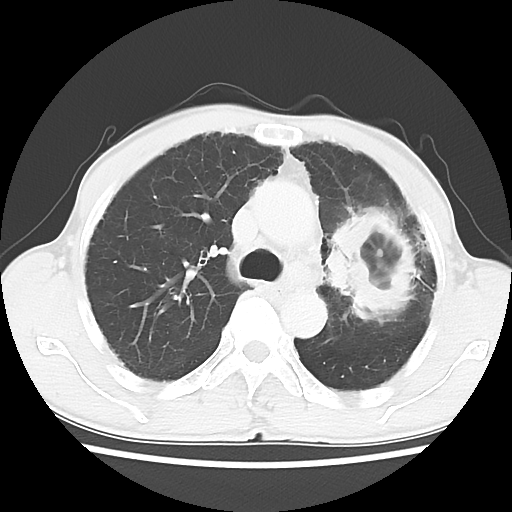
Chest CT, one axial slice; position 41 of 60 along the scan axis; reconstruction kernel LUNG; 120 kVp; lung window (W 1500 / L -600 HU); 5 mm slice thickness; 512 × 512 image matrix, field of view 308 × 308 mm. Male patient, age 64 years. Case-level facts recorded for this patient, not image findings: clinical TNM (as recorded): T3 N3 M0; histopathological grade: G3.
Structures marked on this image (rectangle marked by the reading radiologist):
- lung tumour (recorded histology: adenocarcinoma): bounding box <322,198,417,328> (left, top, right, bottom; pixels)